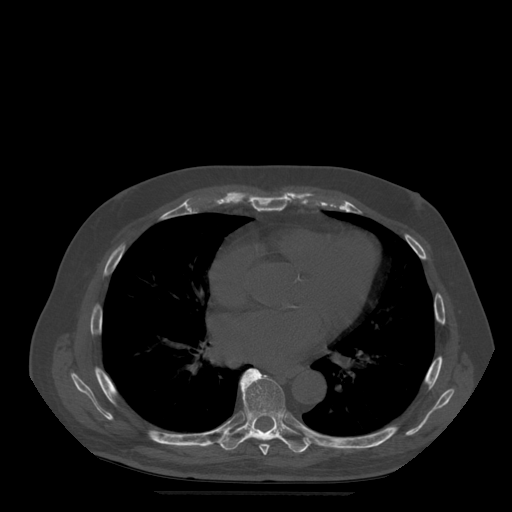
CT including the spine, one axial slice; position 318 of 522 along the scan axis; bone window (W 1800 / L 400 HU); 1.25 mm slice thickness; 512 × 512 image matrix. Patient age 72 years. Case-level facts recorded for this patient, not image findings: primary cancer: prostate.
Structures marked on this image (semi-automatic segmentation, software-assisted and operator-edited):
- T7 vertebra: bounding box [x1, y1, x2, y2] px = [259, 444, 270, 456]
- T8 vertebra: [218, 369, 311, 454]